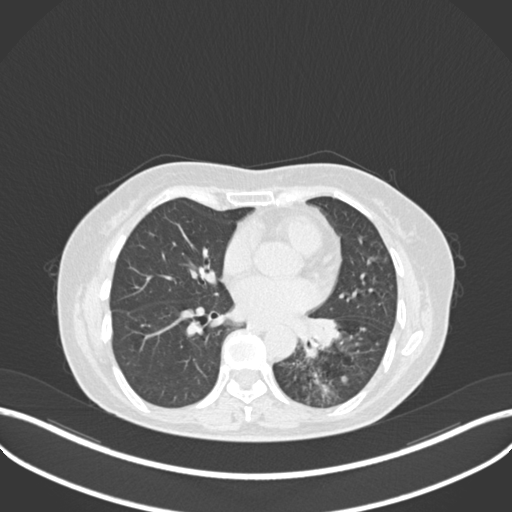
Chest CT, one axial slice. 120 kVp. Lung window (W 1500 / L -600 HU). 1 mm slice thickness. 512 × 512 image matrix. Patient: female, 63 years. Case-level facts recorded for this patient, not image findings: clinical TNM (as recorded): T1b N0 M0; histopathological grade: G2-3.
Outlined on this slice (rectangle marked by the reading radiologist):
- lung tumour (recorded histology: adenocarcinoma): bounding box [x1, y1, x2, y2] px = [292, 311, 345, 361]